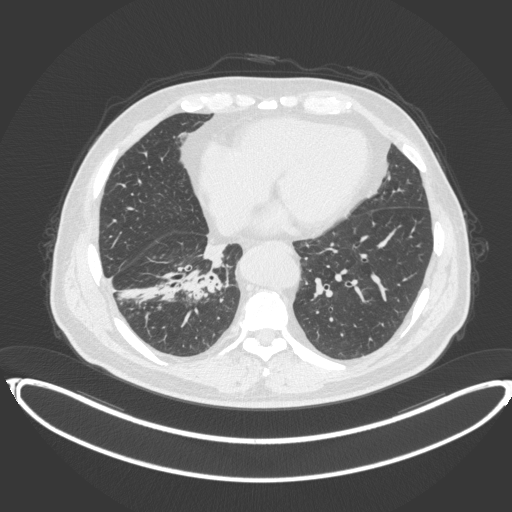
Chest CT, one axial slice; position 143 of 383 along the scan axis; 120 kVp; lung window (W 1500 / L -600 HU); 1 mm slice thickness; 512 × 512 image matrix. Patient: male, 61 years. From the clinical record (not read from this slice): clinical TNM (as recorded): T1b N1 M0.
Structures marked on this image (bounding box drawn by a radiologist):
- lung tumour (recorded histology: squamous cell carcinoma): box from (x=176, y=262) to (x=225, y=302) px